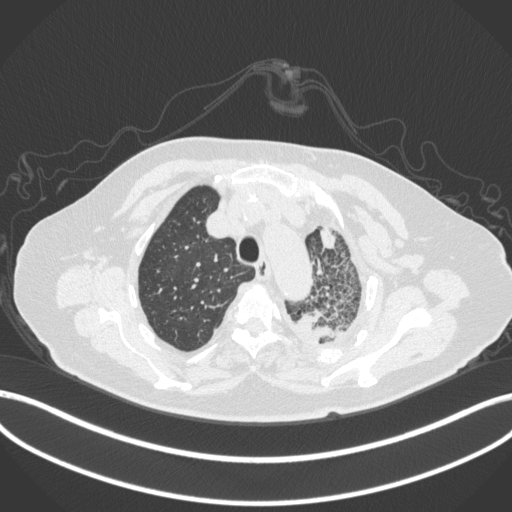
Chest CT, one axial slice. Position 316 of 399 along the scan axis. Reconstruction kernel B31f. Lung window (W 1500 / L -600 HU). 512 × 512 image matrix. Female patient, age 75 years. Case-level facts recorded for this patient, not image findings: clinical TNM (as recorded): T3 N3 M1.
Structures marked on this image (bounding box drawn by a radiologist):
- lung tumour (recorded histology: adenocarcinoma): bounding box <291,303,344,346> (left, top, right, bottom; pixels)